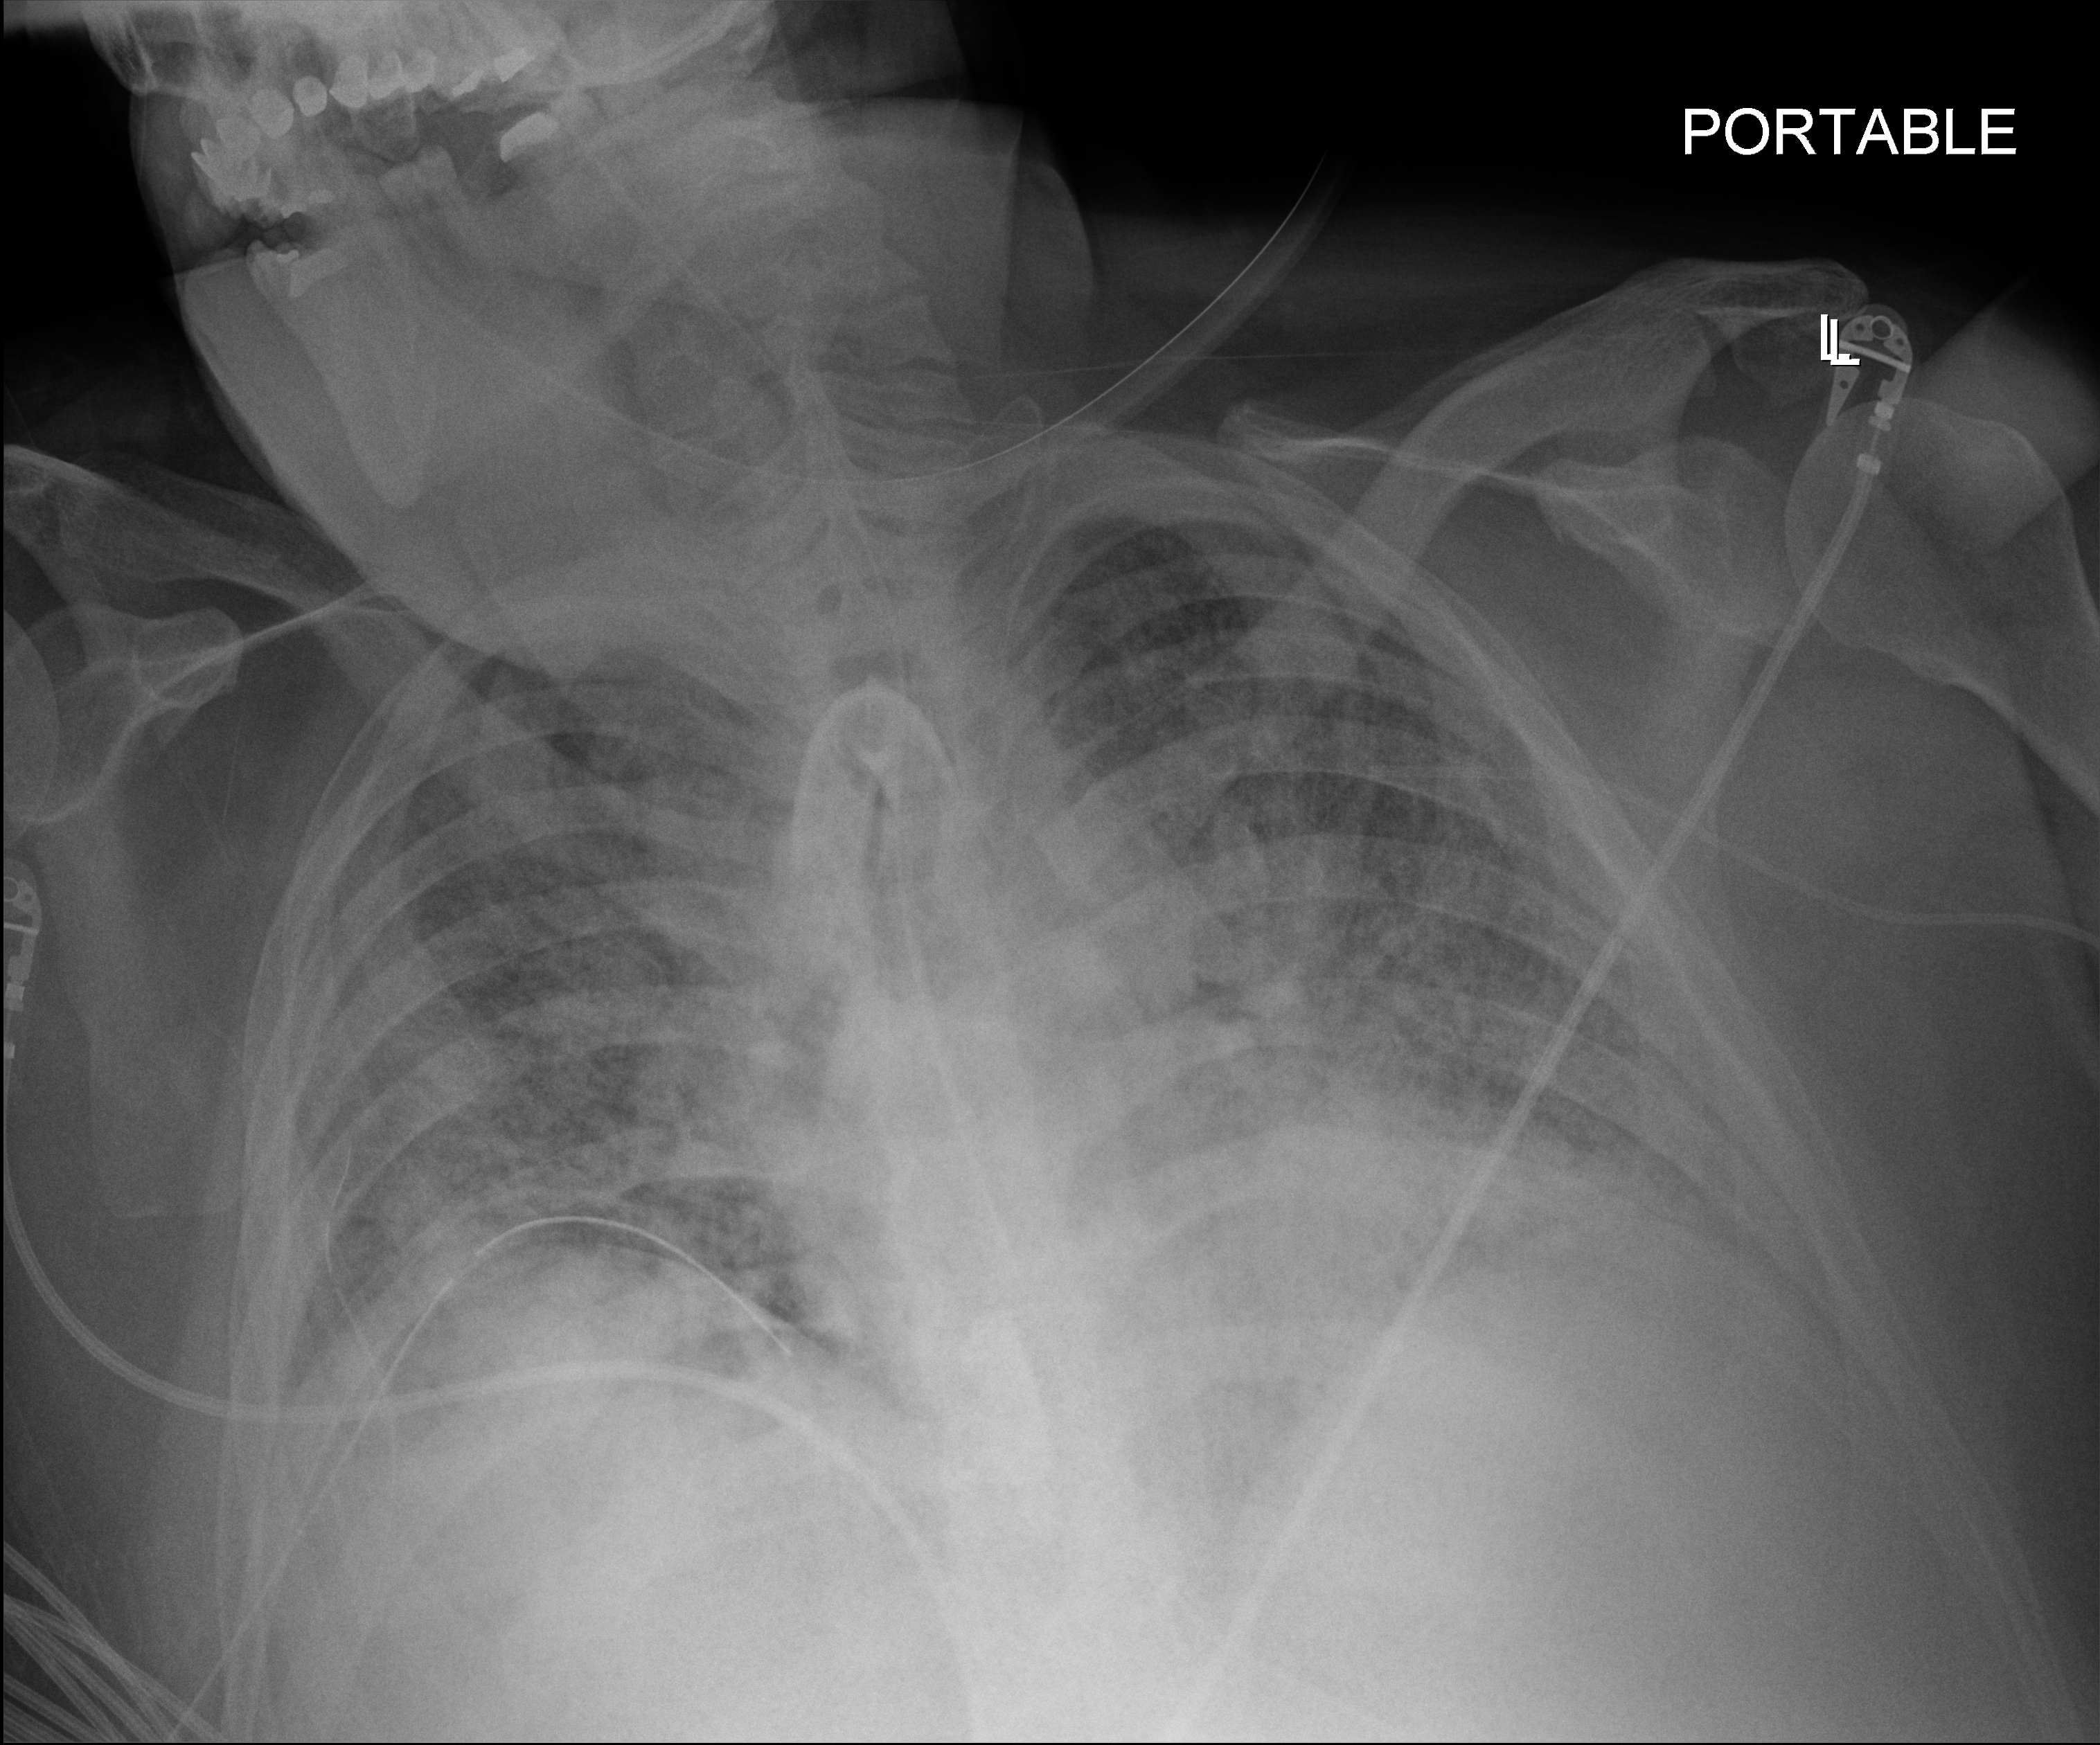
Chest radiograph. Patient hospitalised with COVID-19; male, aged 18–59 years.
Hospital-stay facts (about this admission, not read from this image; timing relative to this image not recorded): mechanically ventilated during this hospital stay: yes.